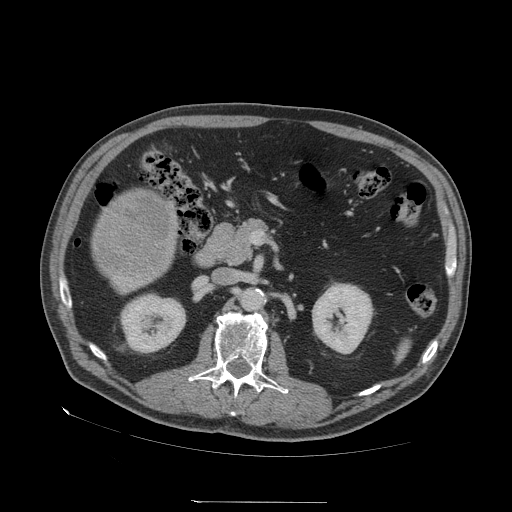
Contrast-enhanced abdominal CT (liver protocol), one axial slice. Position 10 of 83 along the scan axis. Reconstruction kernel STANDARD. 140 kVp. Soft-tissue window (W 400 / L 40 HU). 2.5 mm slice thickness. 512 × 512 image matrix, field of view 460 × 460 mm. From the clinical record (not read from this slice): diagnosis: hepatocellular carcinoma (patient treated with transarterial chemoembolisation; whether this scan precedes or follows treatment is not stated here); TNM stage (as recorded): Stage-I; Child-Pugh class: A.
Outlined on this slice (semi-automatic segmentation, software-assisted and operator-edited):
- mass: box from (x=93, y=190) to (x=179, y=279) px